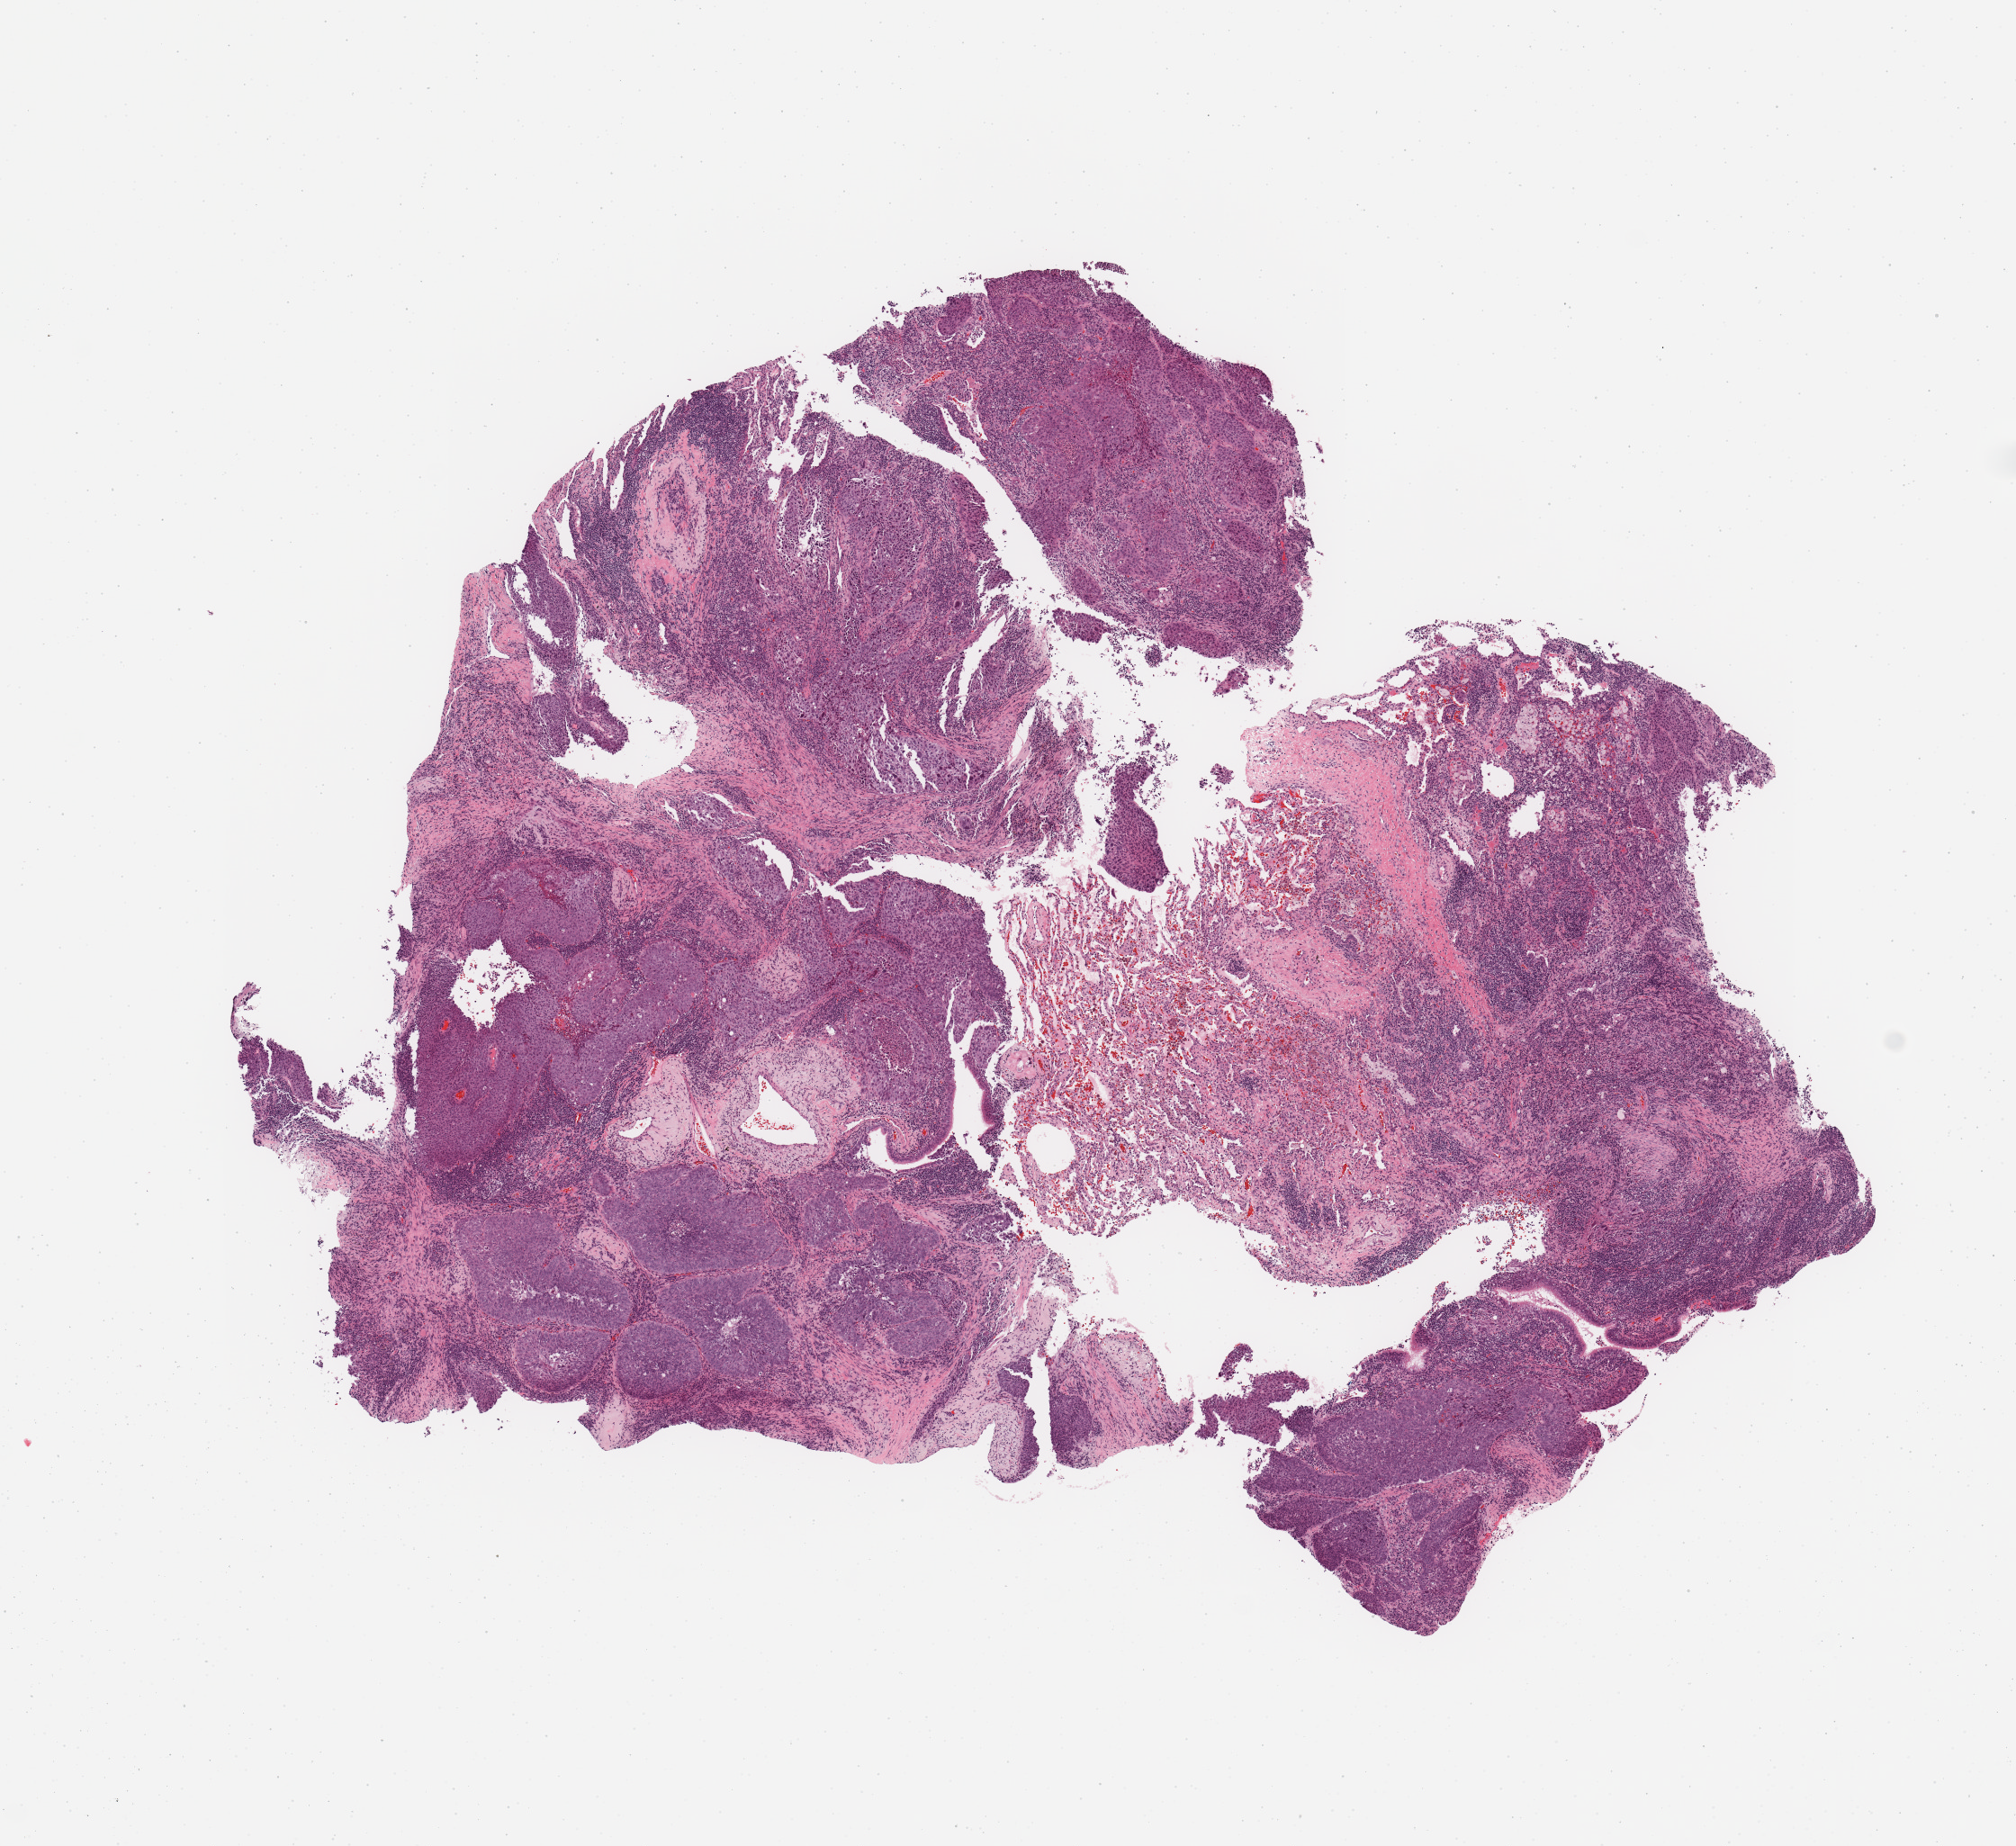
Digitized H&E-stained tissue section (whole slide) — whole scanned area (about 8.9 x 8.1 mm, acquisition: 20x scan) shown as a low-resolution overview, lung, tumour tissue. Female, 66 y/o. Histologic grade: G3 (poorly differentiated).
* AJCC pathologic stage: IIB
* histologic diagnosis: Squamous cell carcinoma, NOS